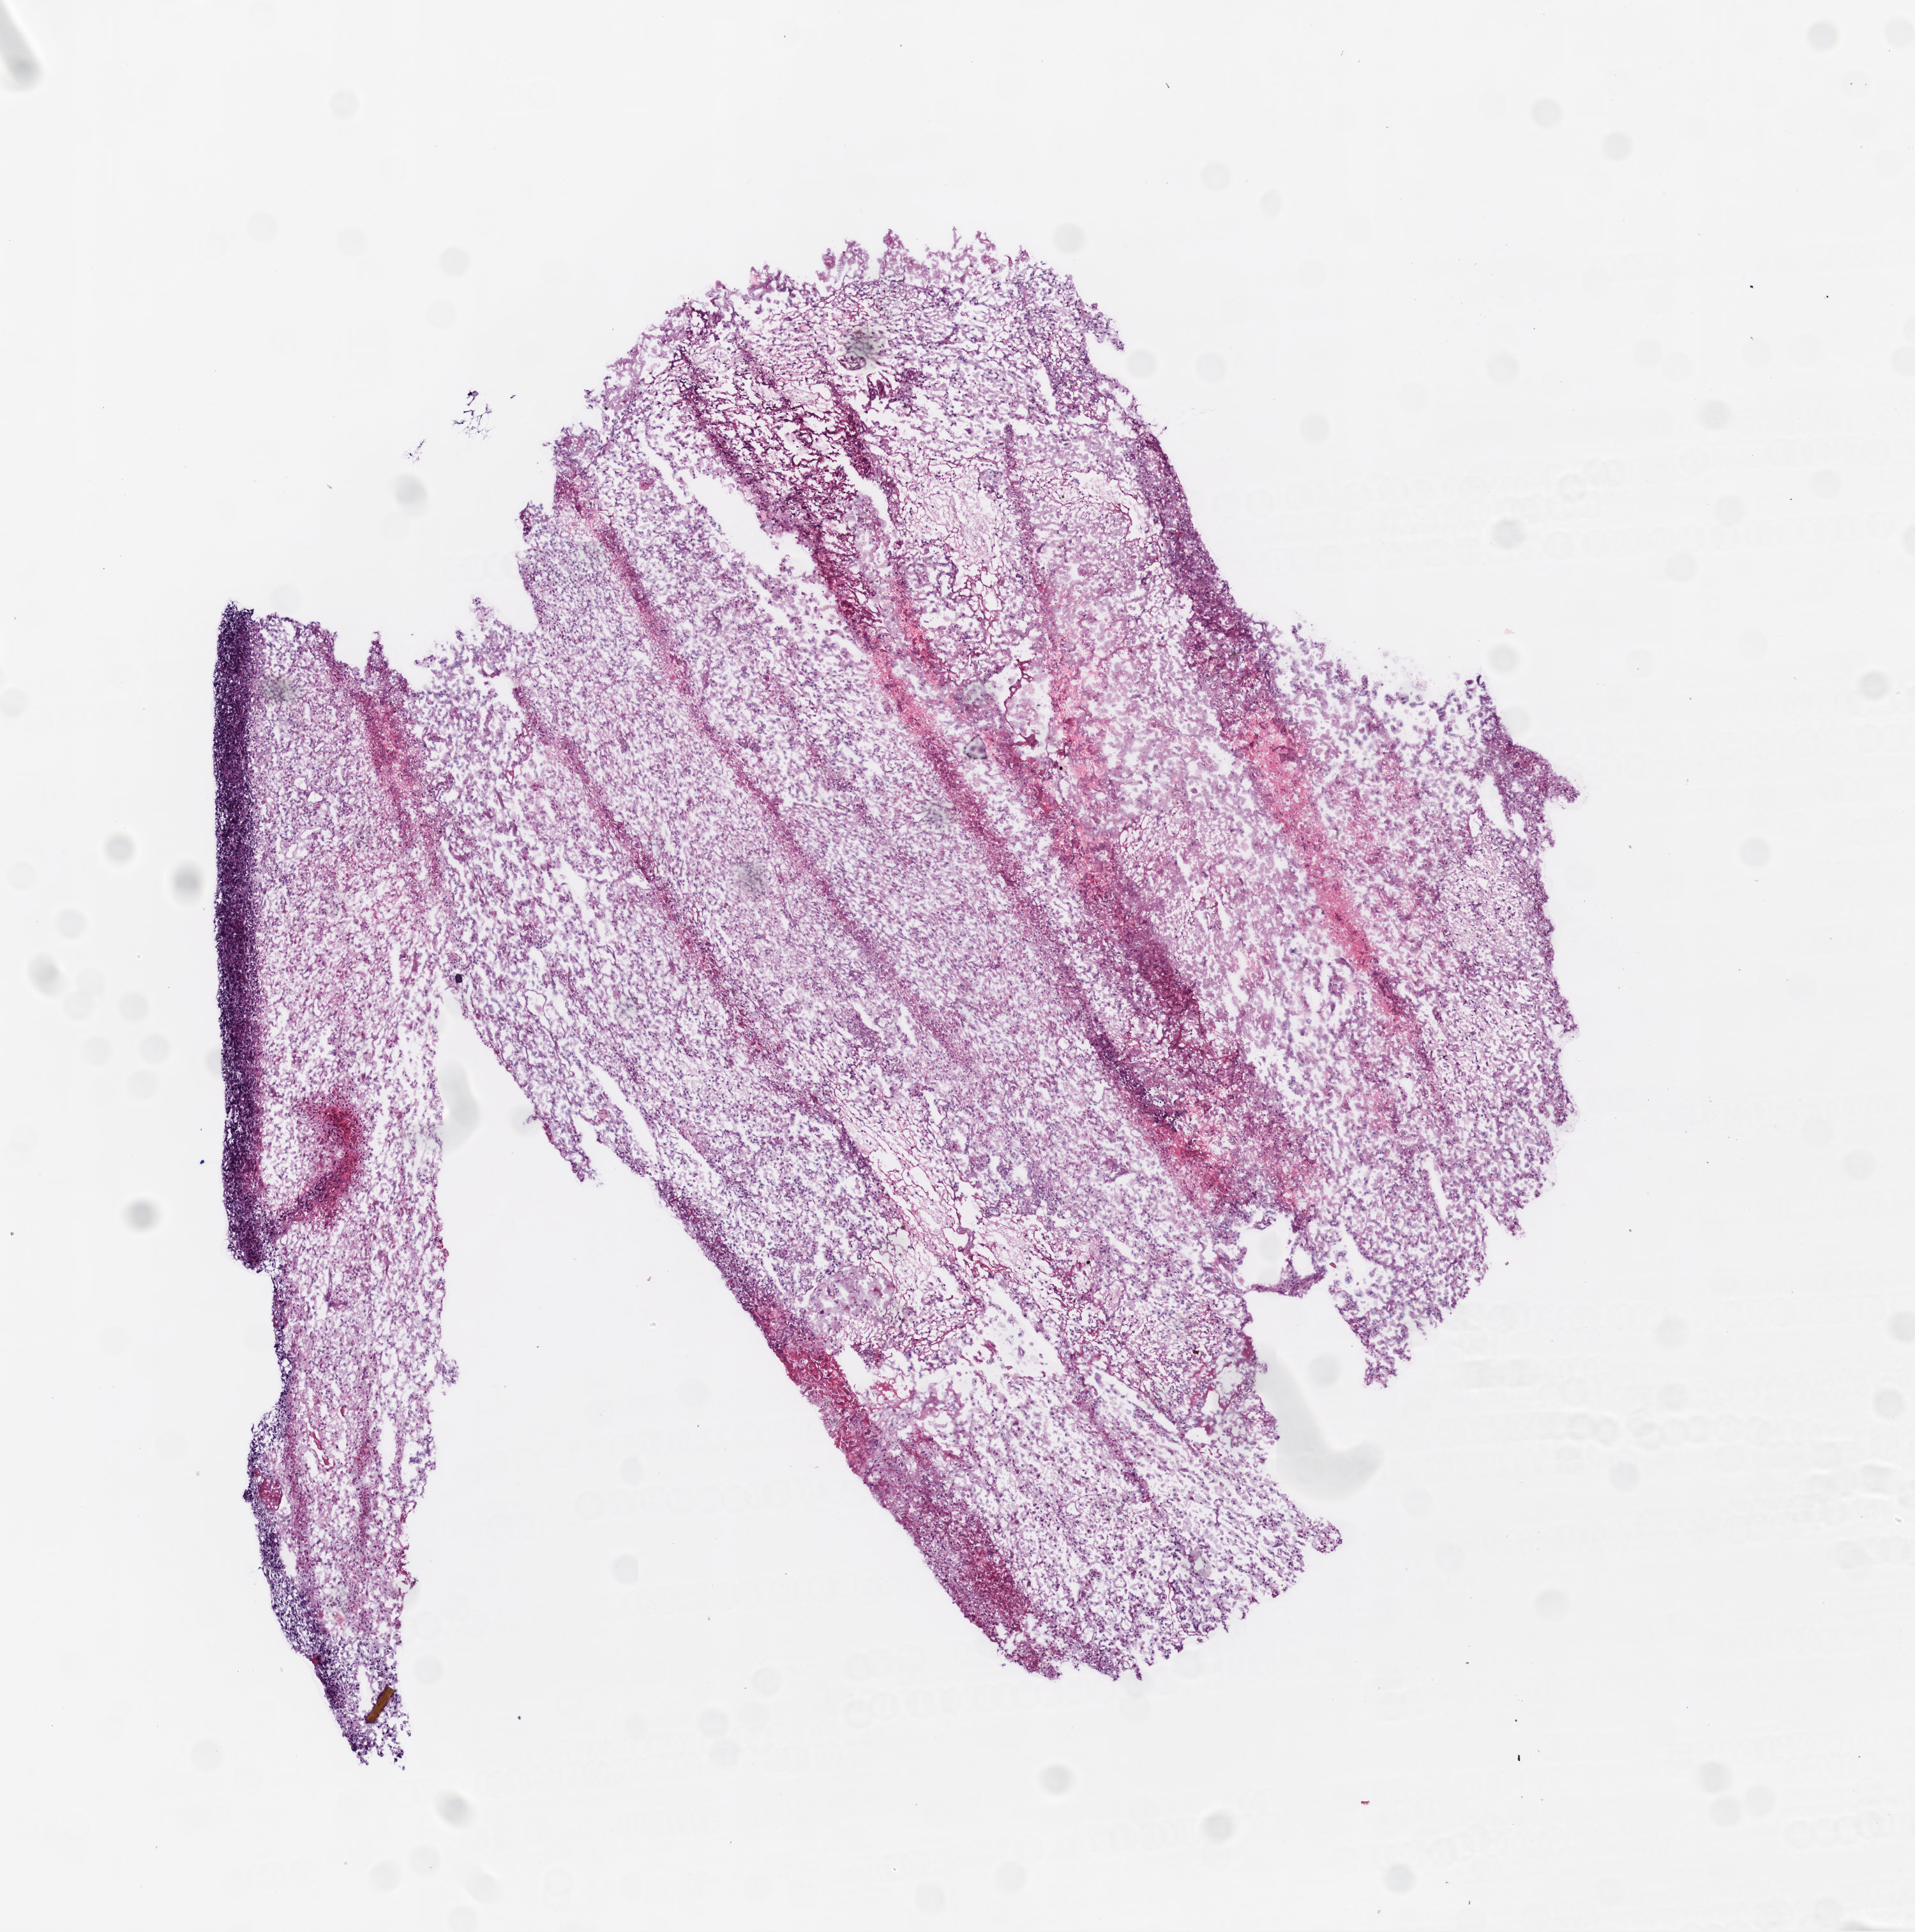
Hematoxylin and eosin (H&E) stained whole-slide image — a low-resolution overview of the entire scanned area, about 6.0 x 6.1 mm (from a 20x scan). Frozen section from the bottom of the tissue portion. Sample: primary tumour, brain. Female, age 55 years at initial diagnosis. Composition of this section per pathologist review: tumour cells 85%, tumour nuclei 85%, normal cells 0%, stromal cells 0%, necrosis 15%.
Histologic diagnosis: Glioblastoma.